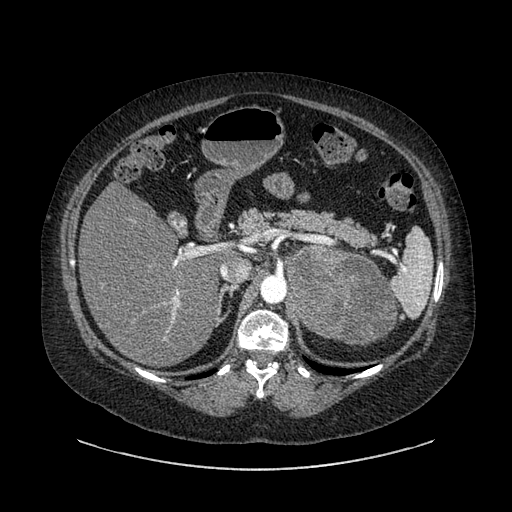
Contrast-enhanced abdominal CT, one axial slice; position 581 of 769 along the scan axis; 120 kVp; intravenous contrast given; soft-tissue window (W 400 / L 40 HU); 0.62 mm slice thickness; 512 × 512 image matrix. Patient: female, 61 years. Case-level facts recorded for this patient, not image findings: diagnosis: adrenocortical carcinoma; tumour side: left adrenal; tumour size at pathology: 13 cm; Ki-67 index: 79 %; stage (as recorded): 2.
Outlined on this slice (semi-automatically segmented with operator editing):
- mass: bounding box [x1, y1, x2, y2] px = [288, 247, 394, 345]